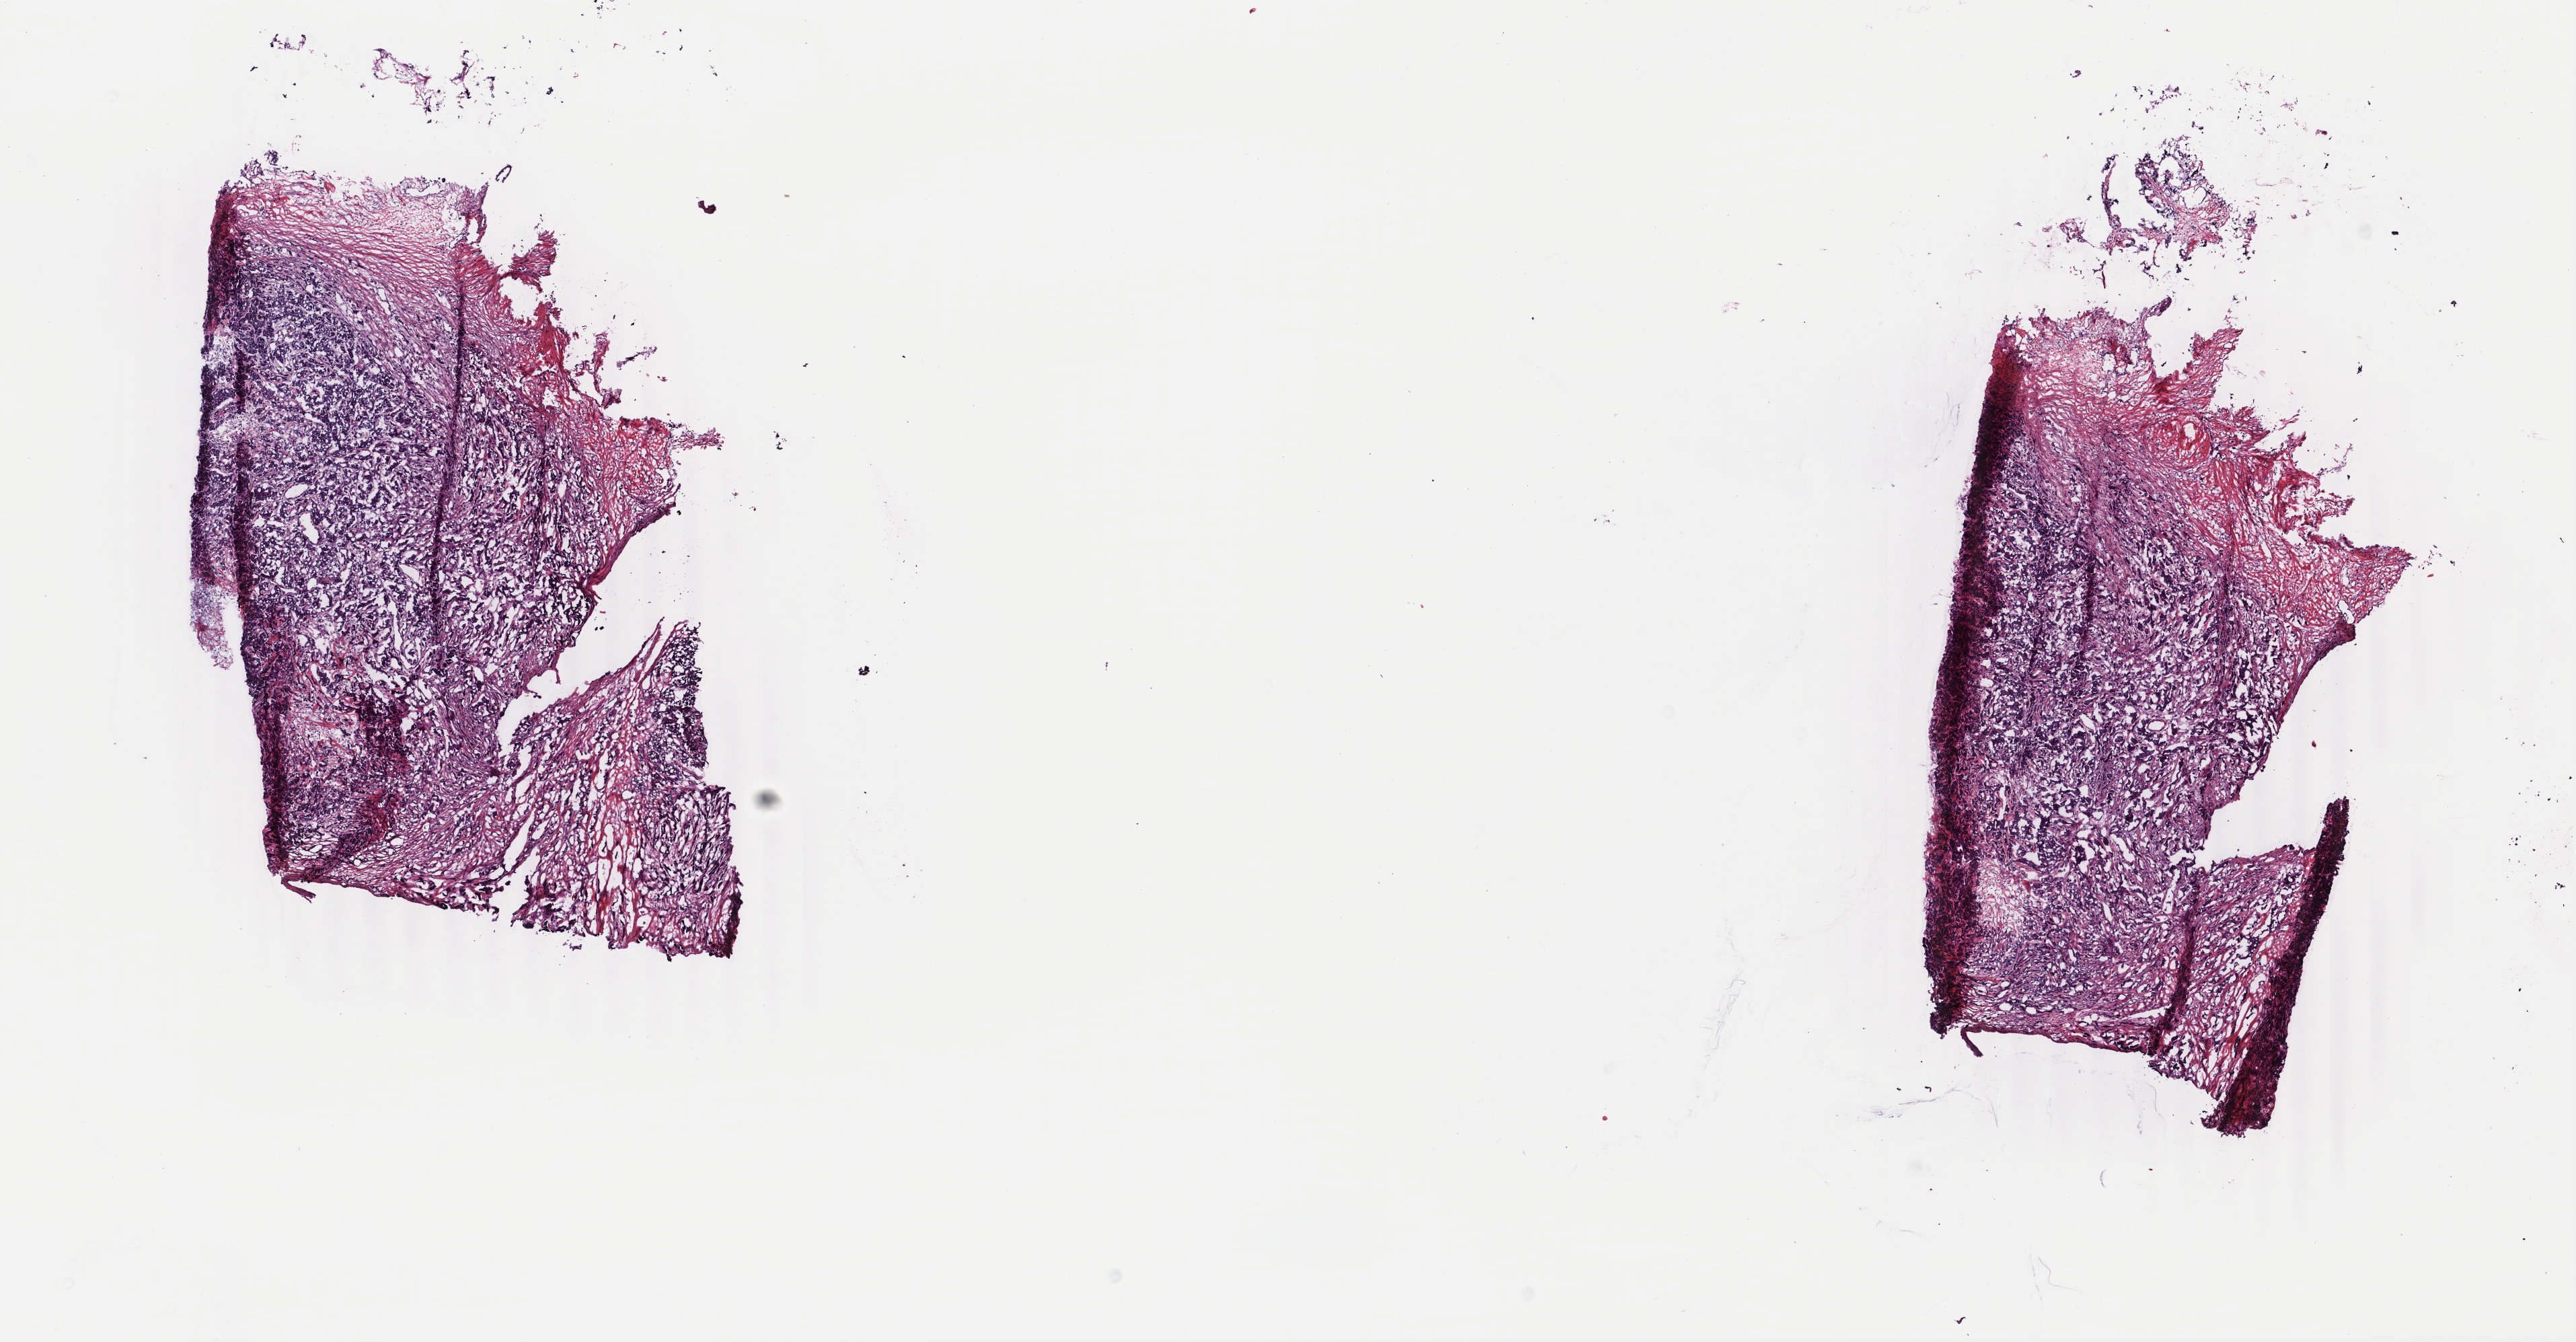
Digitized H&E-stained tissue section (whole slide) — low-resolution overview of the scanned area, about 15.2 x 7.9 mm (acquisition: 40x scan), frozen section from the top of the tissue portion, sample: primary tumour, breast. Patient: female, age at initial diagnosis 64 years. Composition of this section per pathologist review: tumour cells 85%, tumour nuclei 85%, normal cells 0%, stromal cells 15%, necrosis 0%. Inflammatory infiltration, as recorded: lymphocyte infiltration 2%, monocyte infiltration 0%, neutrophil infiltration 0%.
Histologic diagnosis: Infiltrating duct carcinoma, NOS. Laterality: right. Lymph nodes positive (case pathology): 8 of 15 examined. AJCC pathologic stage: IV.